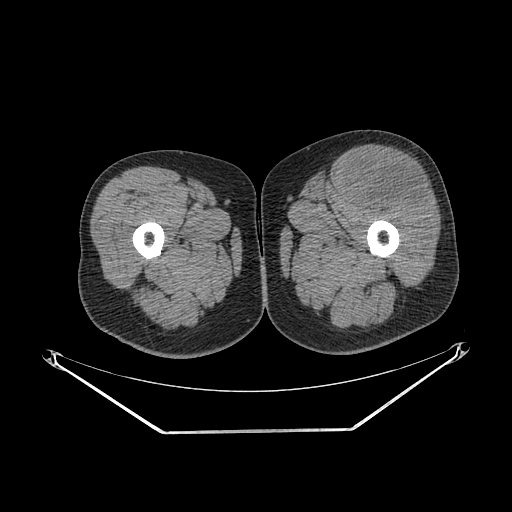
CT of an extremity soft-tissue mass (from a PET/CT study), one axial slice; slice 240 of 267 in the series (ordered by position); soft-tissue window (W 400 / L 40 HU); 3.75 mm slice thickness; 512 × 512 image matrix. Male patient. From the clinical record (not read from this slice): histological type: extraskeletal osteosarcoma; grade: high; site of the primary tumour: thigh.
Annotated regions visible in this slice (expert contour drawn on MRI and transferred to this co-registered scan by the dataset authors):
- gross tumour volume (mass): bounding box (x1, y1, x2, y2) in pixels: (352, 160, 428, 211)